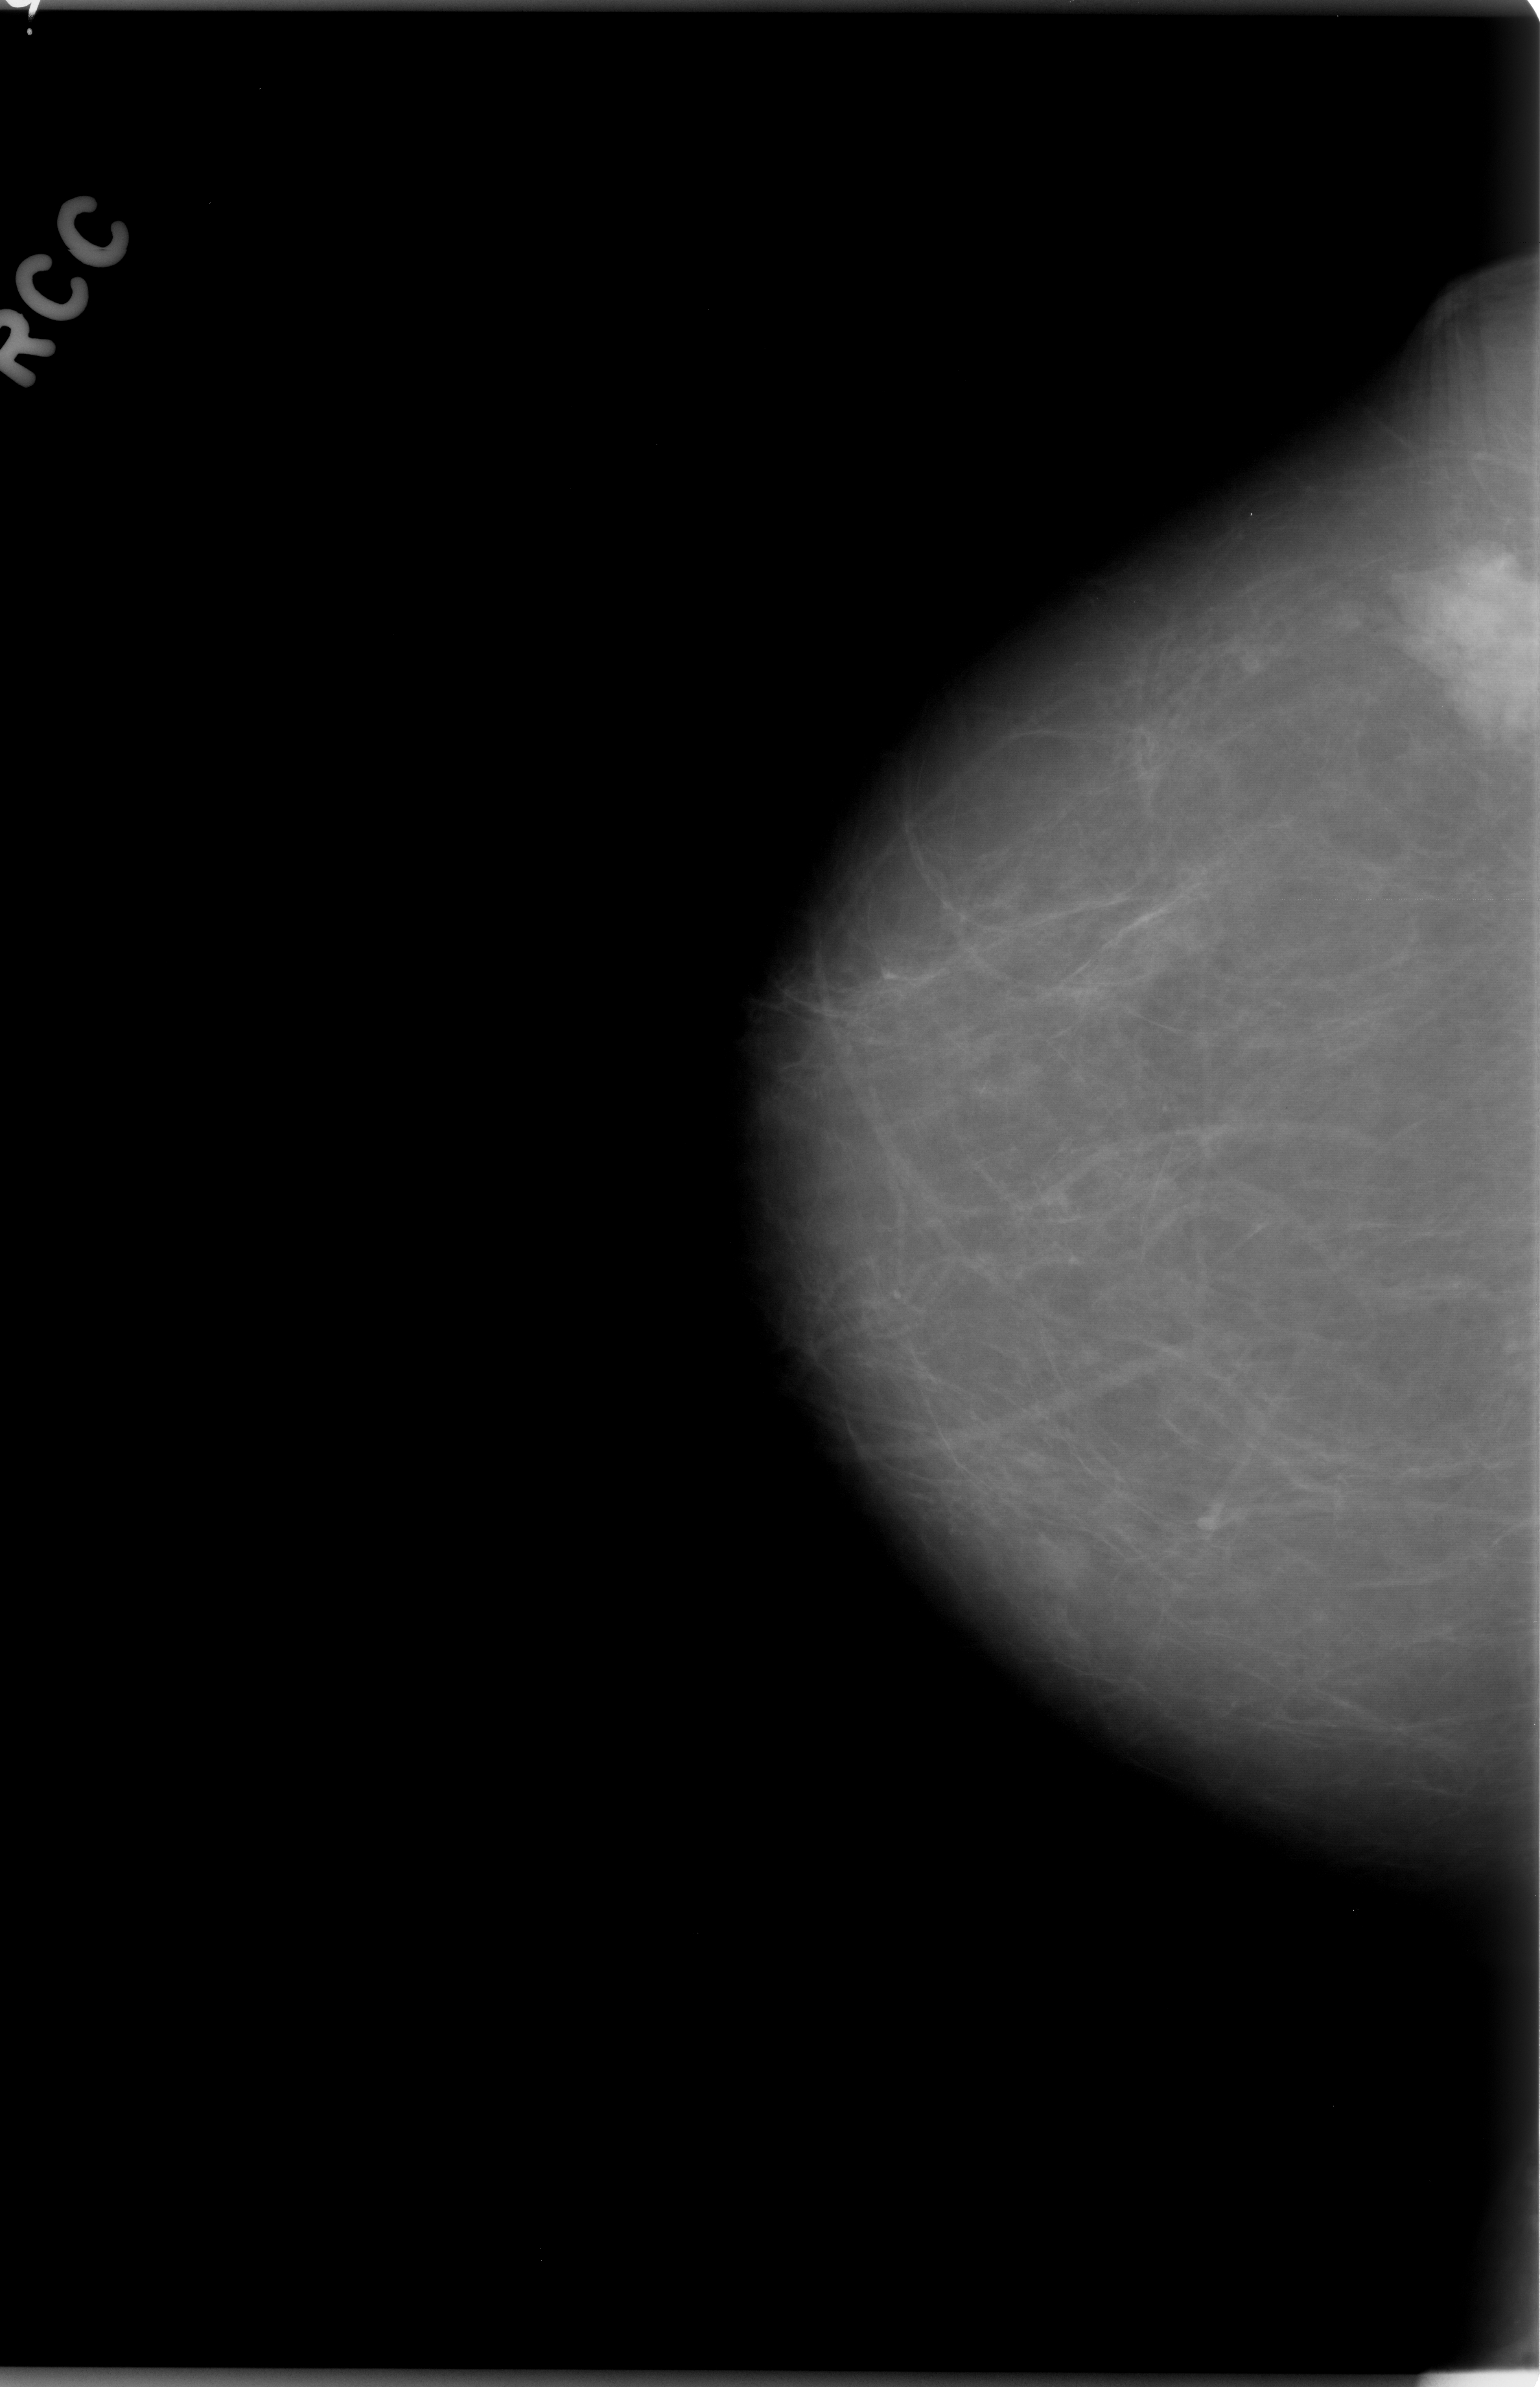
Digitized screen-film mammogram. Right breast. Craniocaudal (CC) view. Breast composition: almost entirely fatty (BI-RADS density category 1 of 4). 1540 × 2387 image matrix.
Expert-marked regions of interest on this image (one box per marked abnormality):
- mass, shape lobulated, margins microlobulated; BI-RADS assessment category 5; subtlety rating 5 on a 1 (subtle) to 5 (obvious) scale; pathology result (as recorded, not read from the image): malignant: bounding box (x1, y1, x2, y2) in pixels: (1369, 497, 1540, 765)